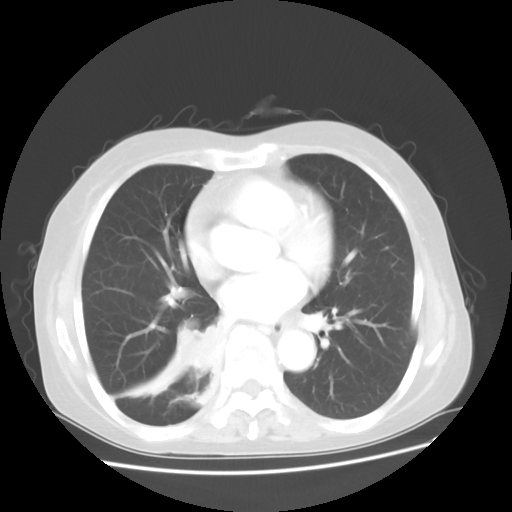
Chest CT, one axial slice. Position 20 of 48 along the scan axis. Reconstruction kernel STANDARD. Lung window (W 1500 / L -600 HU). 5 mm slice thickness. 512 × 512 image matrix, field of view 360 × 360 mm. Patient: female, 63 years. From the clinical record (not read from this slice): clinical TNM (as recorded): T2 N3 M1b.
Structures marked on this image (bounding box drawn by a radiologist):
- lung tumour (recorded histology: small cell carcinoma): box from (x=170, y=316) to (x=221, y=375) px